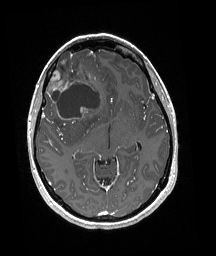
Brain MRI from a brain-tumour surgery series, one axial slice; slice 108 of 192 in the series (ordered by position); T1-weighted post-contrast; 1 mm slice thickness; 216 × 256 image matrix, field of view 211 × 250 mm. Case-level facts recorded for this patient, not image findings: histopathology: Oligodendroglioma; WHO grade: 3; IDH mutation: yes; tumour location: Right Frontal.
Annotated regions visible in this slice (outlined manually by an expert reader):
- tumour: bounding box [x1, y1, x2, y2] px = [47, 51, 100, 125]